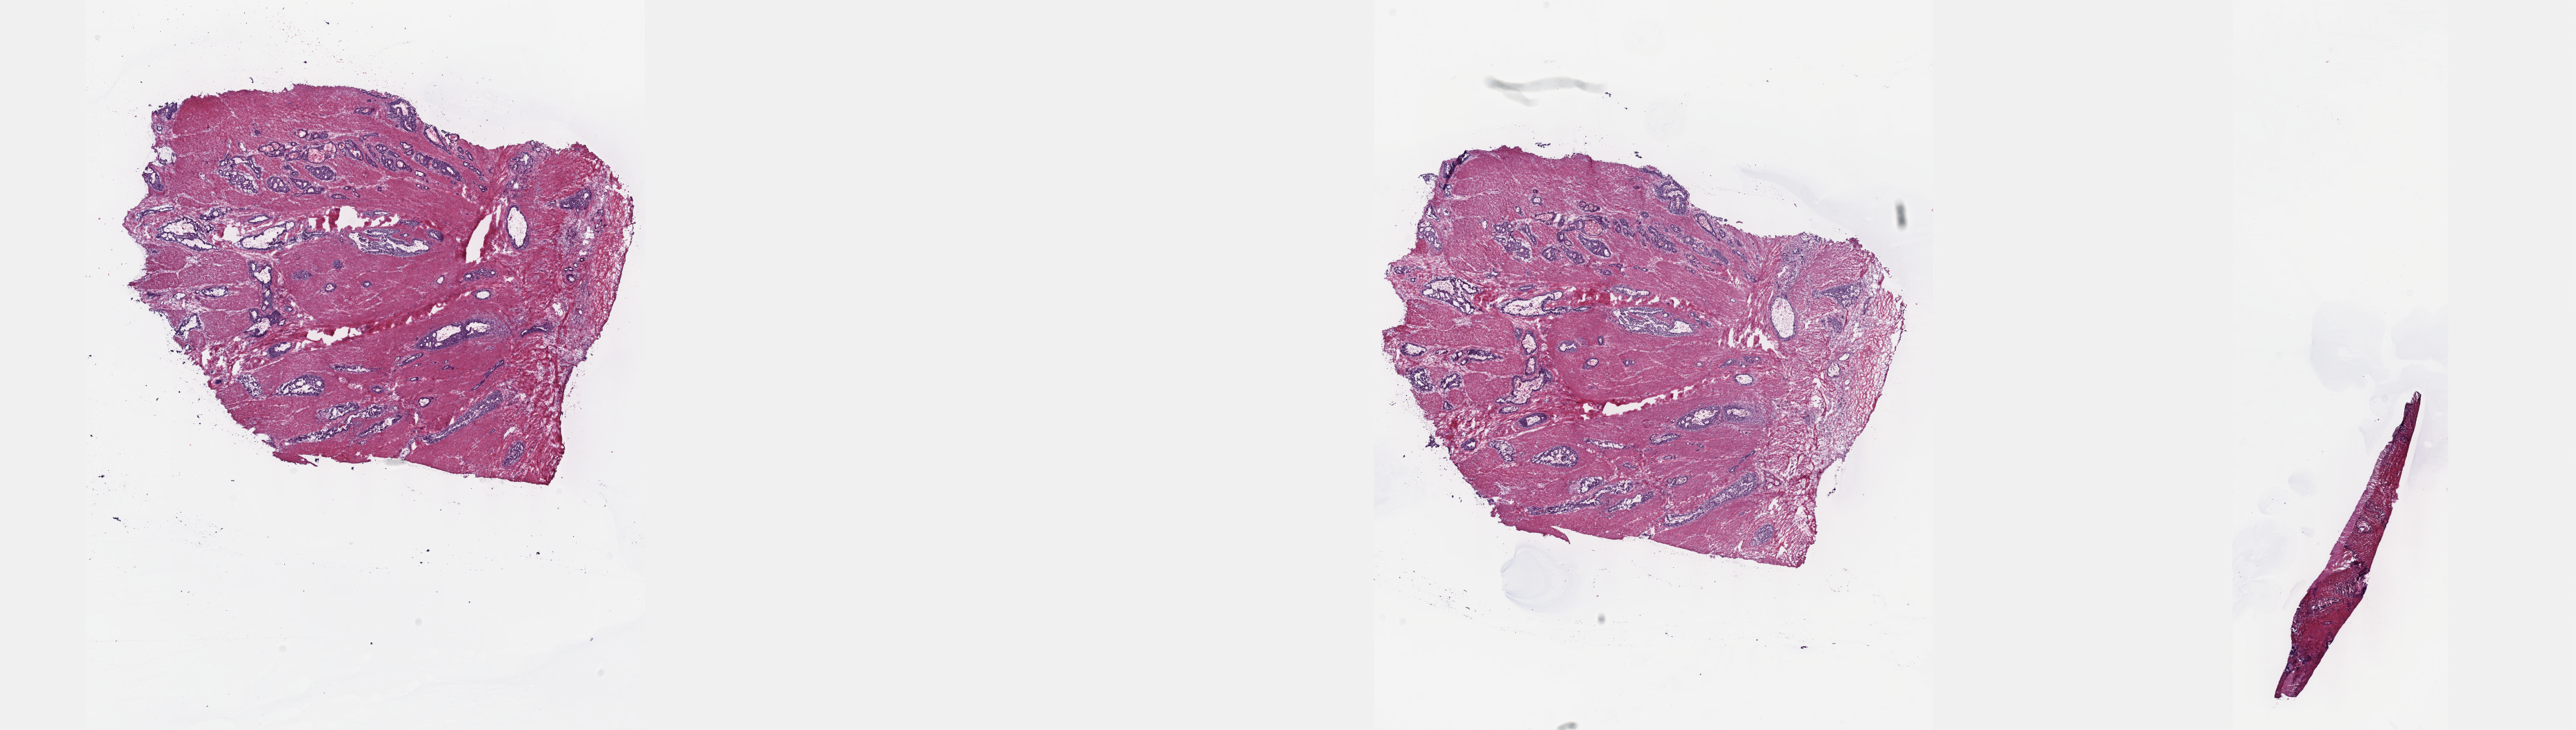
Hematoxylin and eosin (H&E) stained whole-slide image — a low-resolution overview of the entire scanned area, about 30.2 x 8.6 mm; frozen section from the top of the tissue portion; primary tumour sample from the stomach. Female patient; age at initial diagnosis 78 years. Histologic grade: G3 (poorly differentiated). Composition of this section per pathologist review: tumour cells 100%, tumour nuclei 60%, normal cells 0%, stromal cells 0%, necrosis 0%. Infiltration values recorded for this section: lymphocyte infiltration 3%, monocyte infiltration 0%, neutrophil infiltration 0%.
Diagnosis: Adenocarcinoma, intestinal type (gastric antrum). AJCC pathologic stage: IIIA.